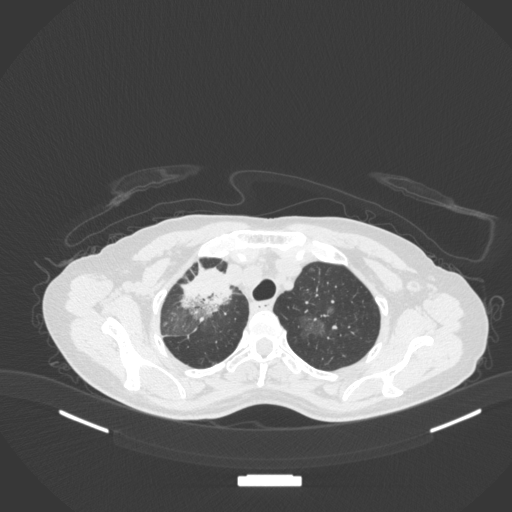
Chest CT, one axial slice. Position 269 of 311 along the scan axis. Reconstruction kernel B31f. 120 kVp. Lung window (W 1500 / L -600 HU). 1 mm slice thickness. 512 × 512 image matrix, field of view 400 × 400 mm. Patient: female, 59 years. From the clinical record (not read from this slice): clinical TNM (as recorded): T3 N0 M0; histopathological grade: G1.
Structures marked on this image (rectangle marked by the reading radiologist):
- lung tumour (recorded histology: adenocarcinoma): bounding box [x1, y1, x2, y2] px = [175, 253, 241, 324]